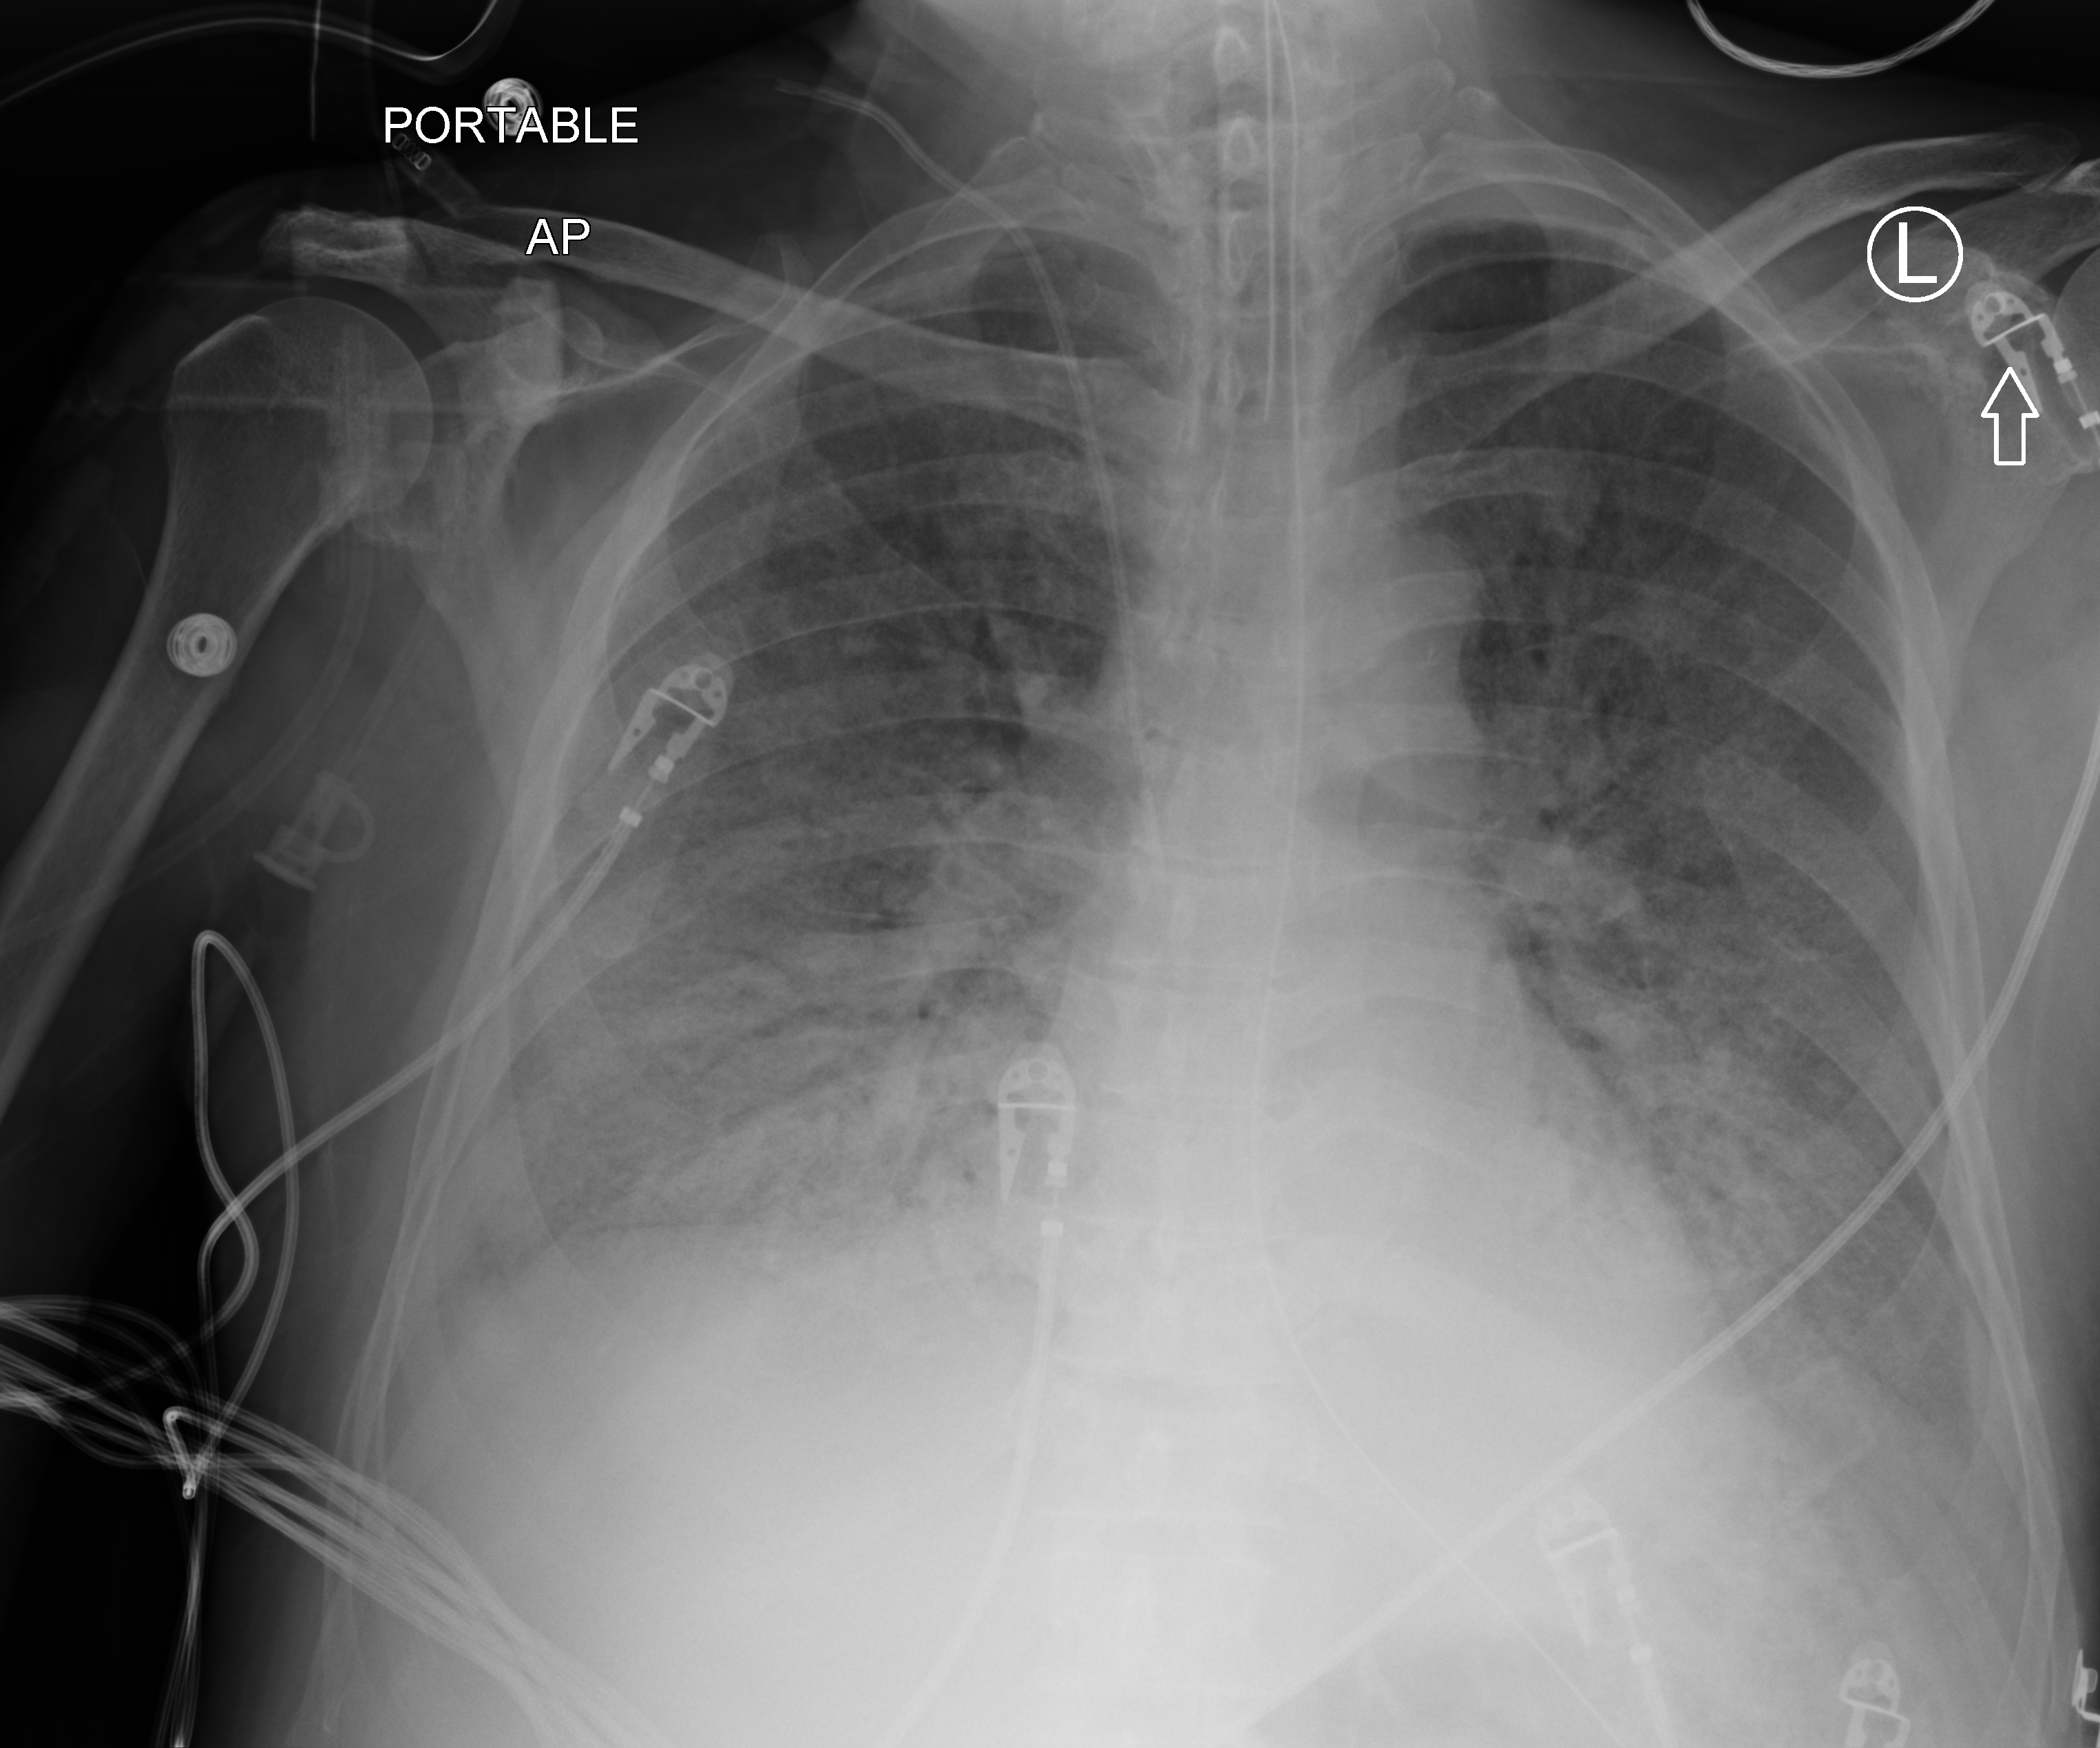
Chest X-ray (portable); anteroposterior (AP) projection. Male patient hospitalised with COVID-19, age 60–74 years.
Admission-level facts for this patient (not findings on this image; timing relative to this image not recorded): mechanically ventilated during this hospital stay: yes.